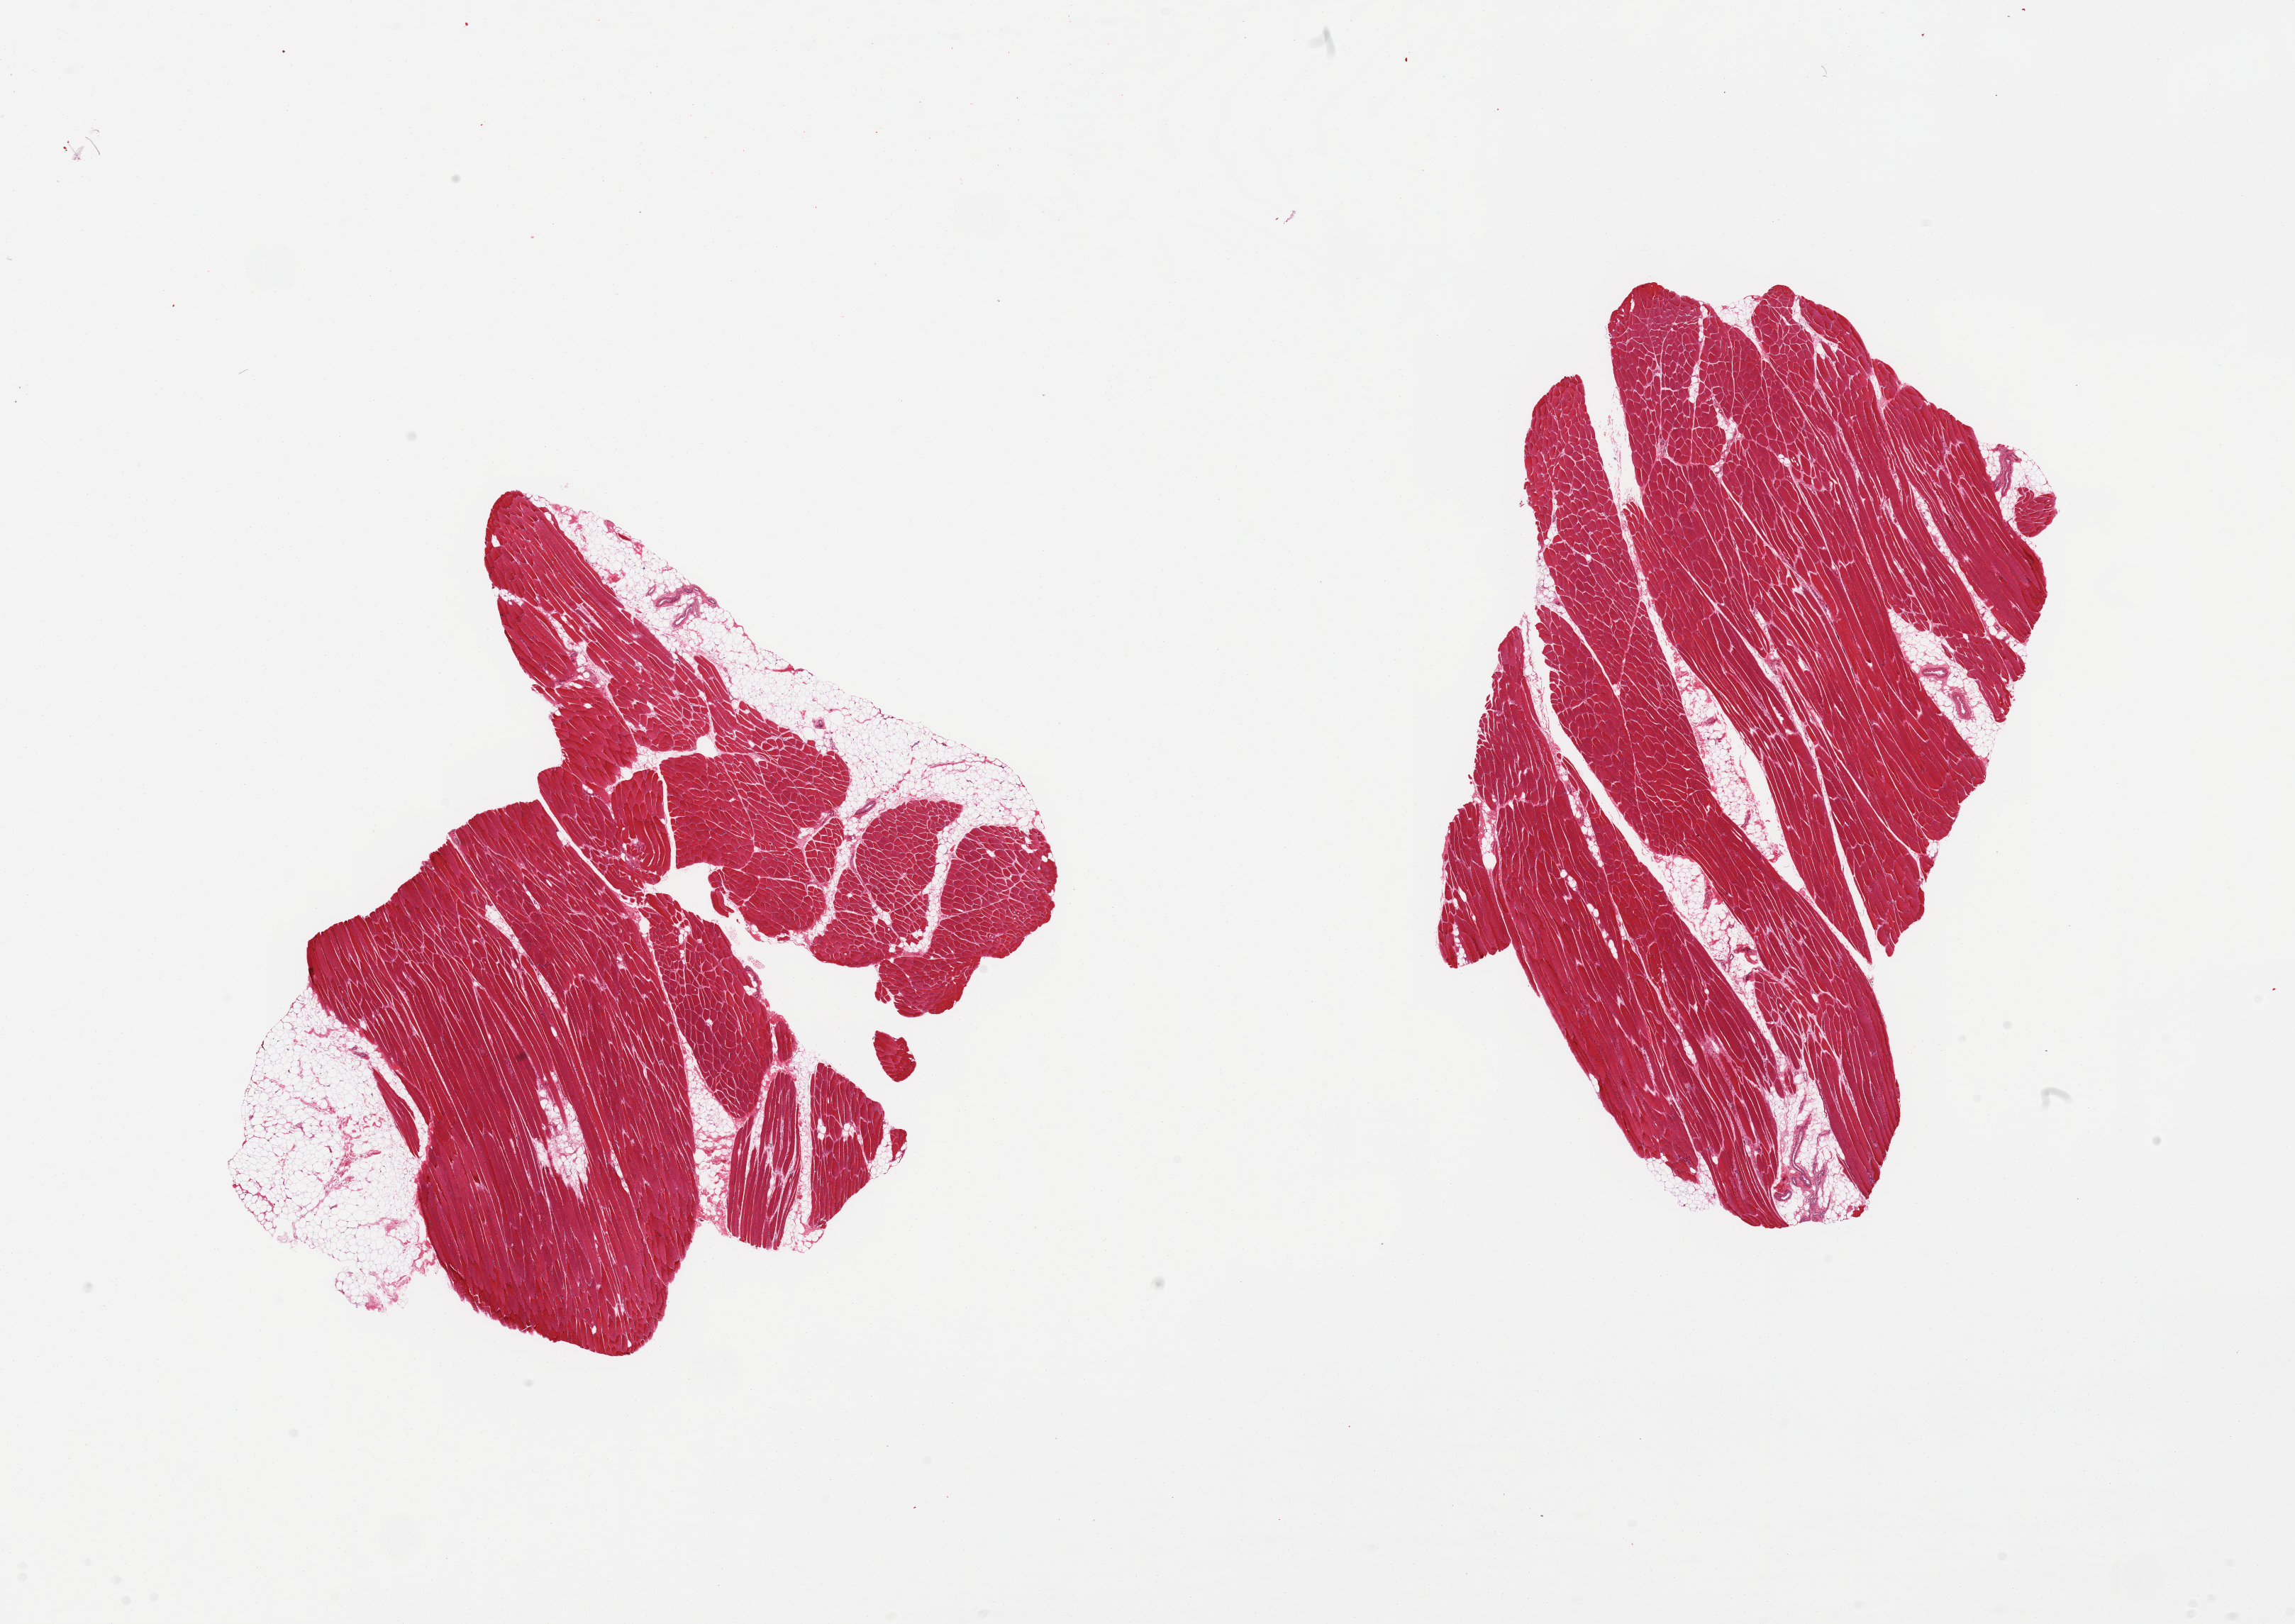
Whole-slide image, H&E stain, brightfield, low-resolution overview of the scanned area, about 25.6 x 18.1 mm. PAXgene-fixed, paraffin-embedded tissue. Section of skeletal muscle (target tissue). Donor tissue sample.
Reviewer comment on this tissue sample: 2 pieces, ~10-15% interstitial fat.